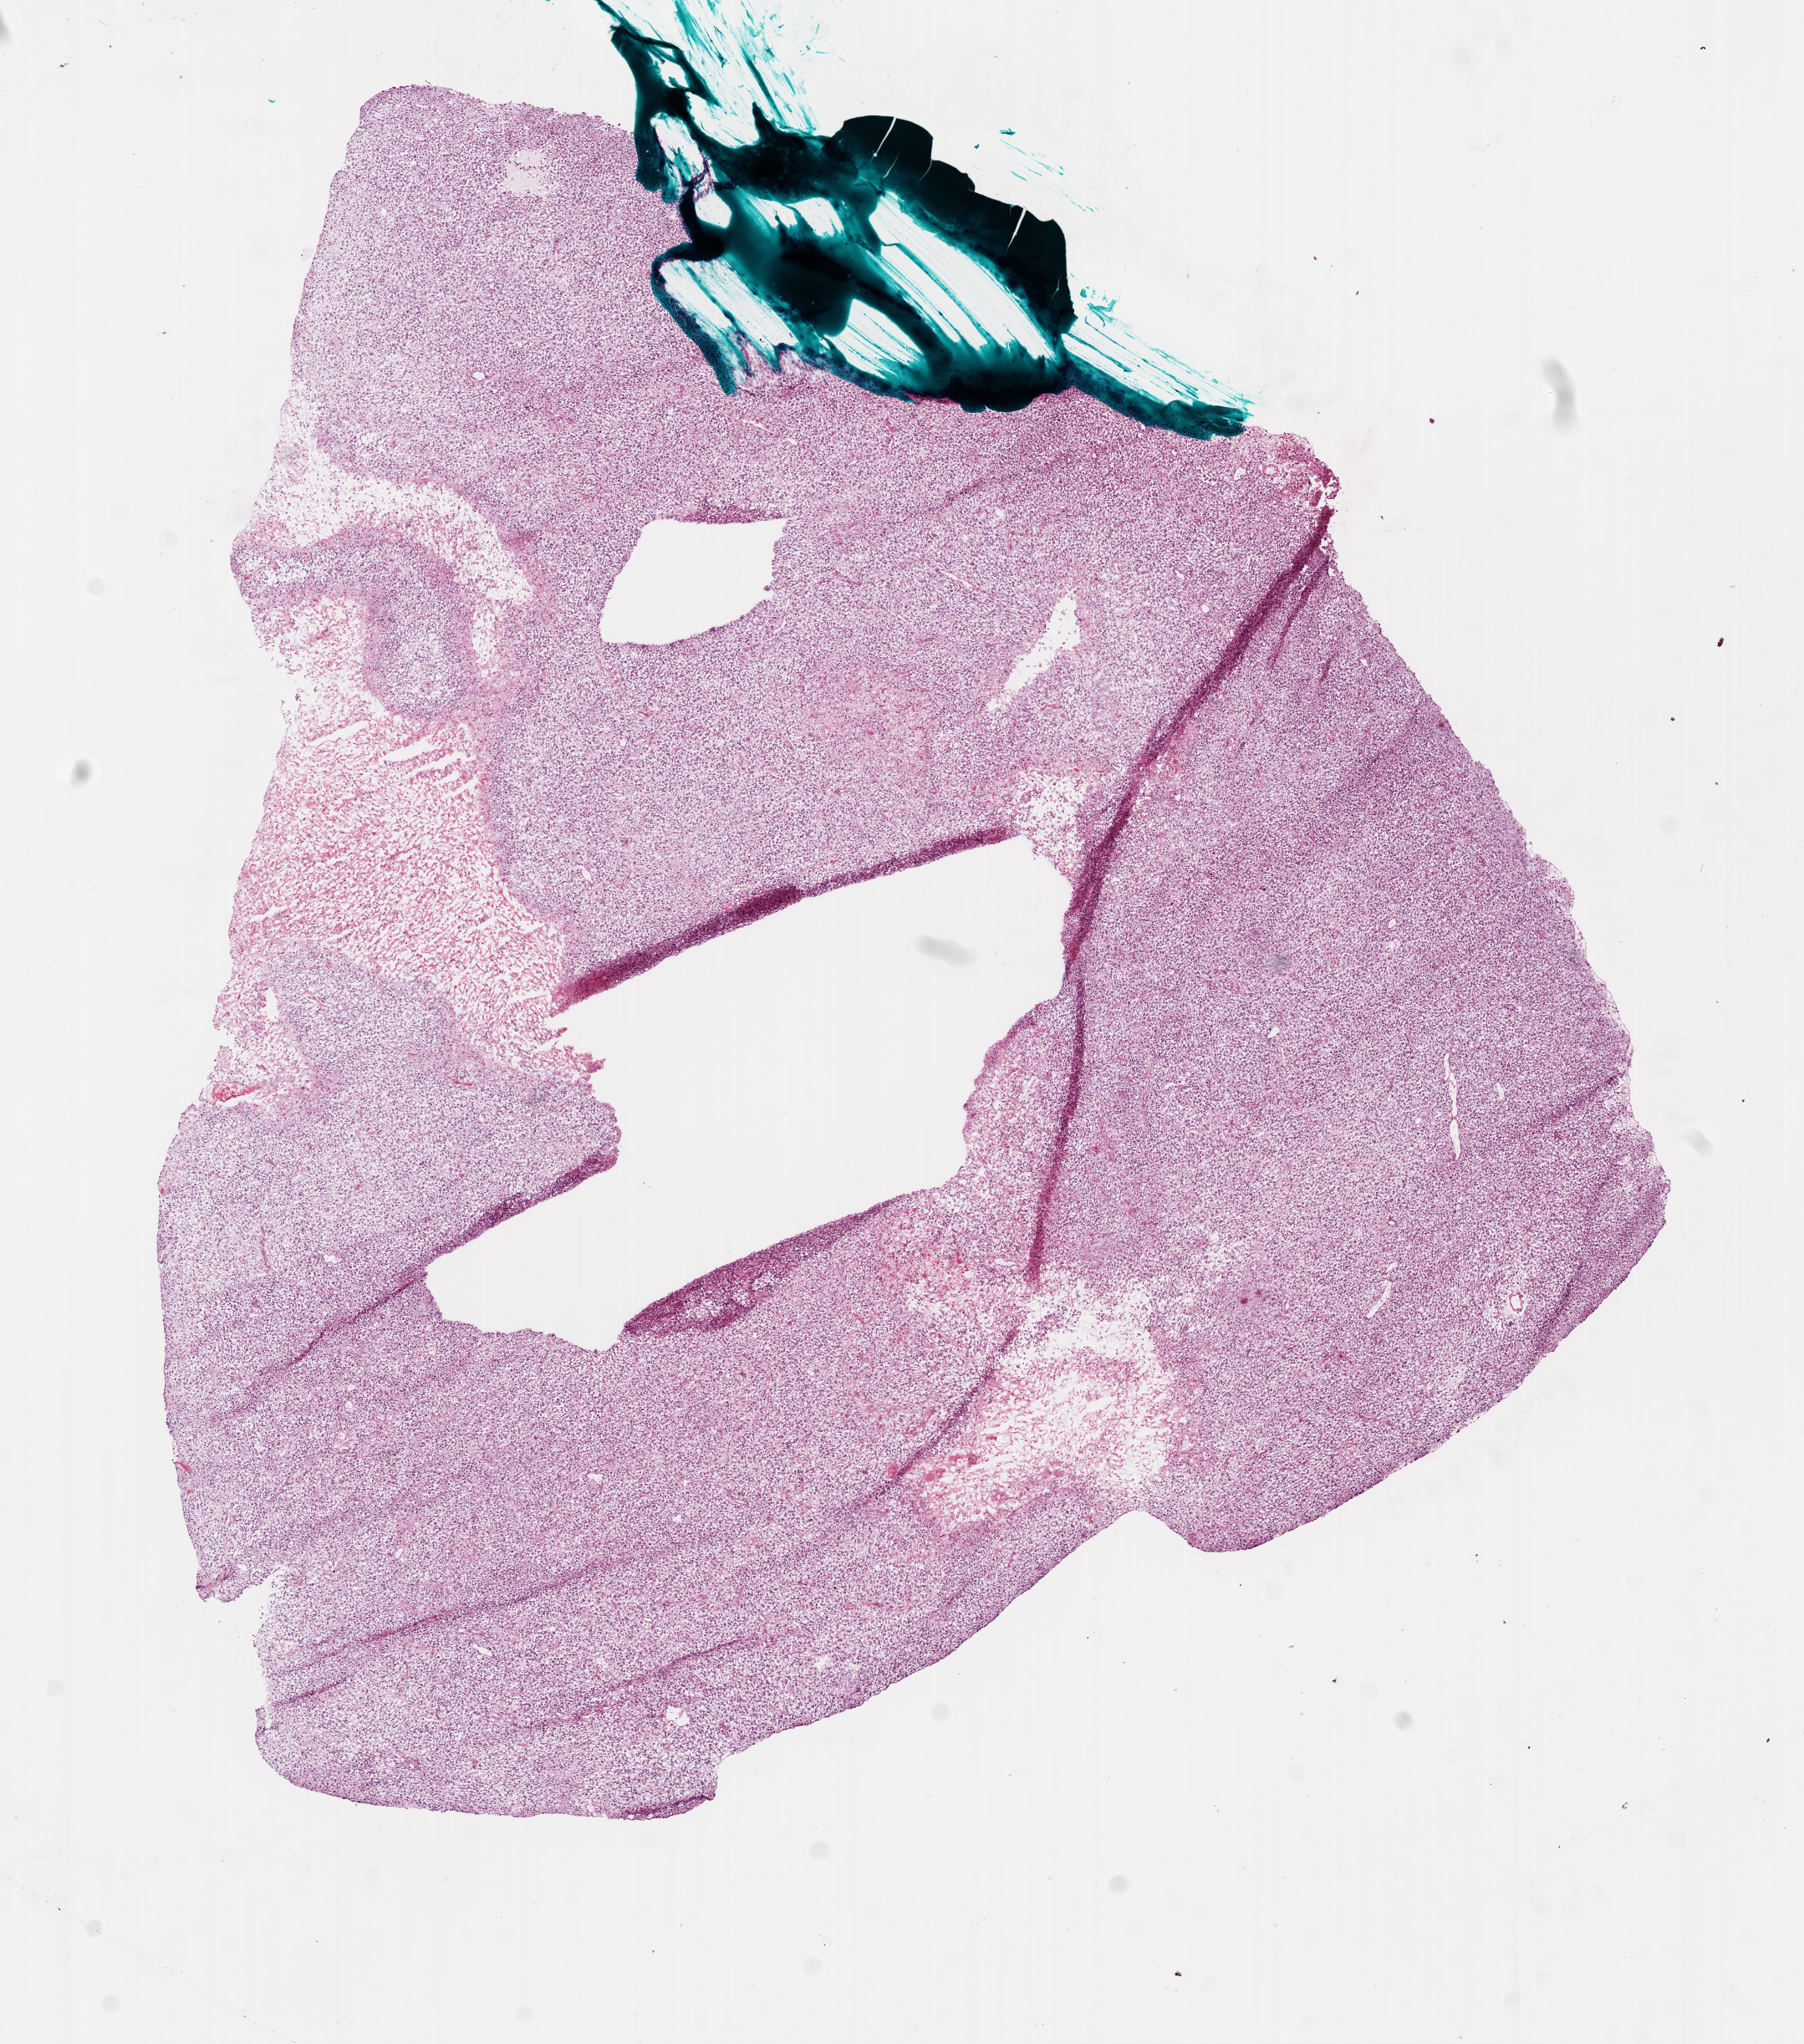
H&E-stained whole-slide image, shown as a low-resolution overview of the whole scanned area (about 8.7 x 9.9 mm, acquisition: 20x scan), frozen section, sample: primary tumour, brain. Patient: male, age at initial diagnosis 52 years. Composition of this section per pathologist review: tumour cells 85%, tumour nuclei 100%, normal cells 0%, stromal cells 0%, necrosis 15%.
• pathologic diagnosis: Glioblastoma